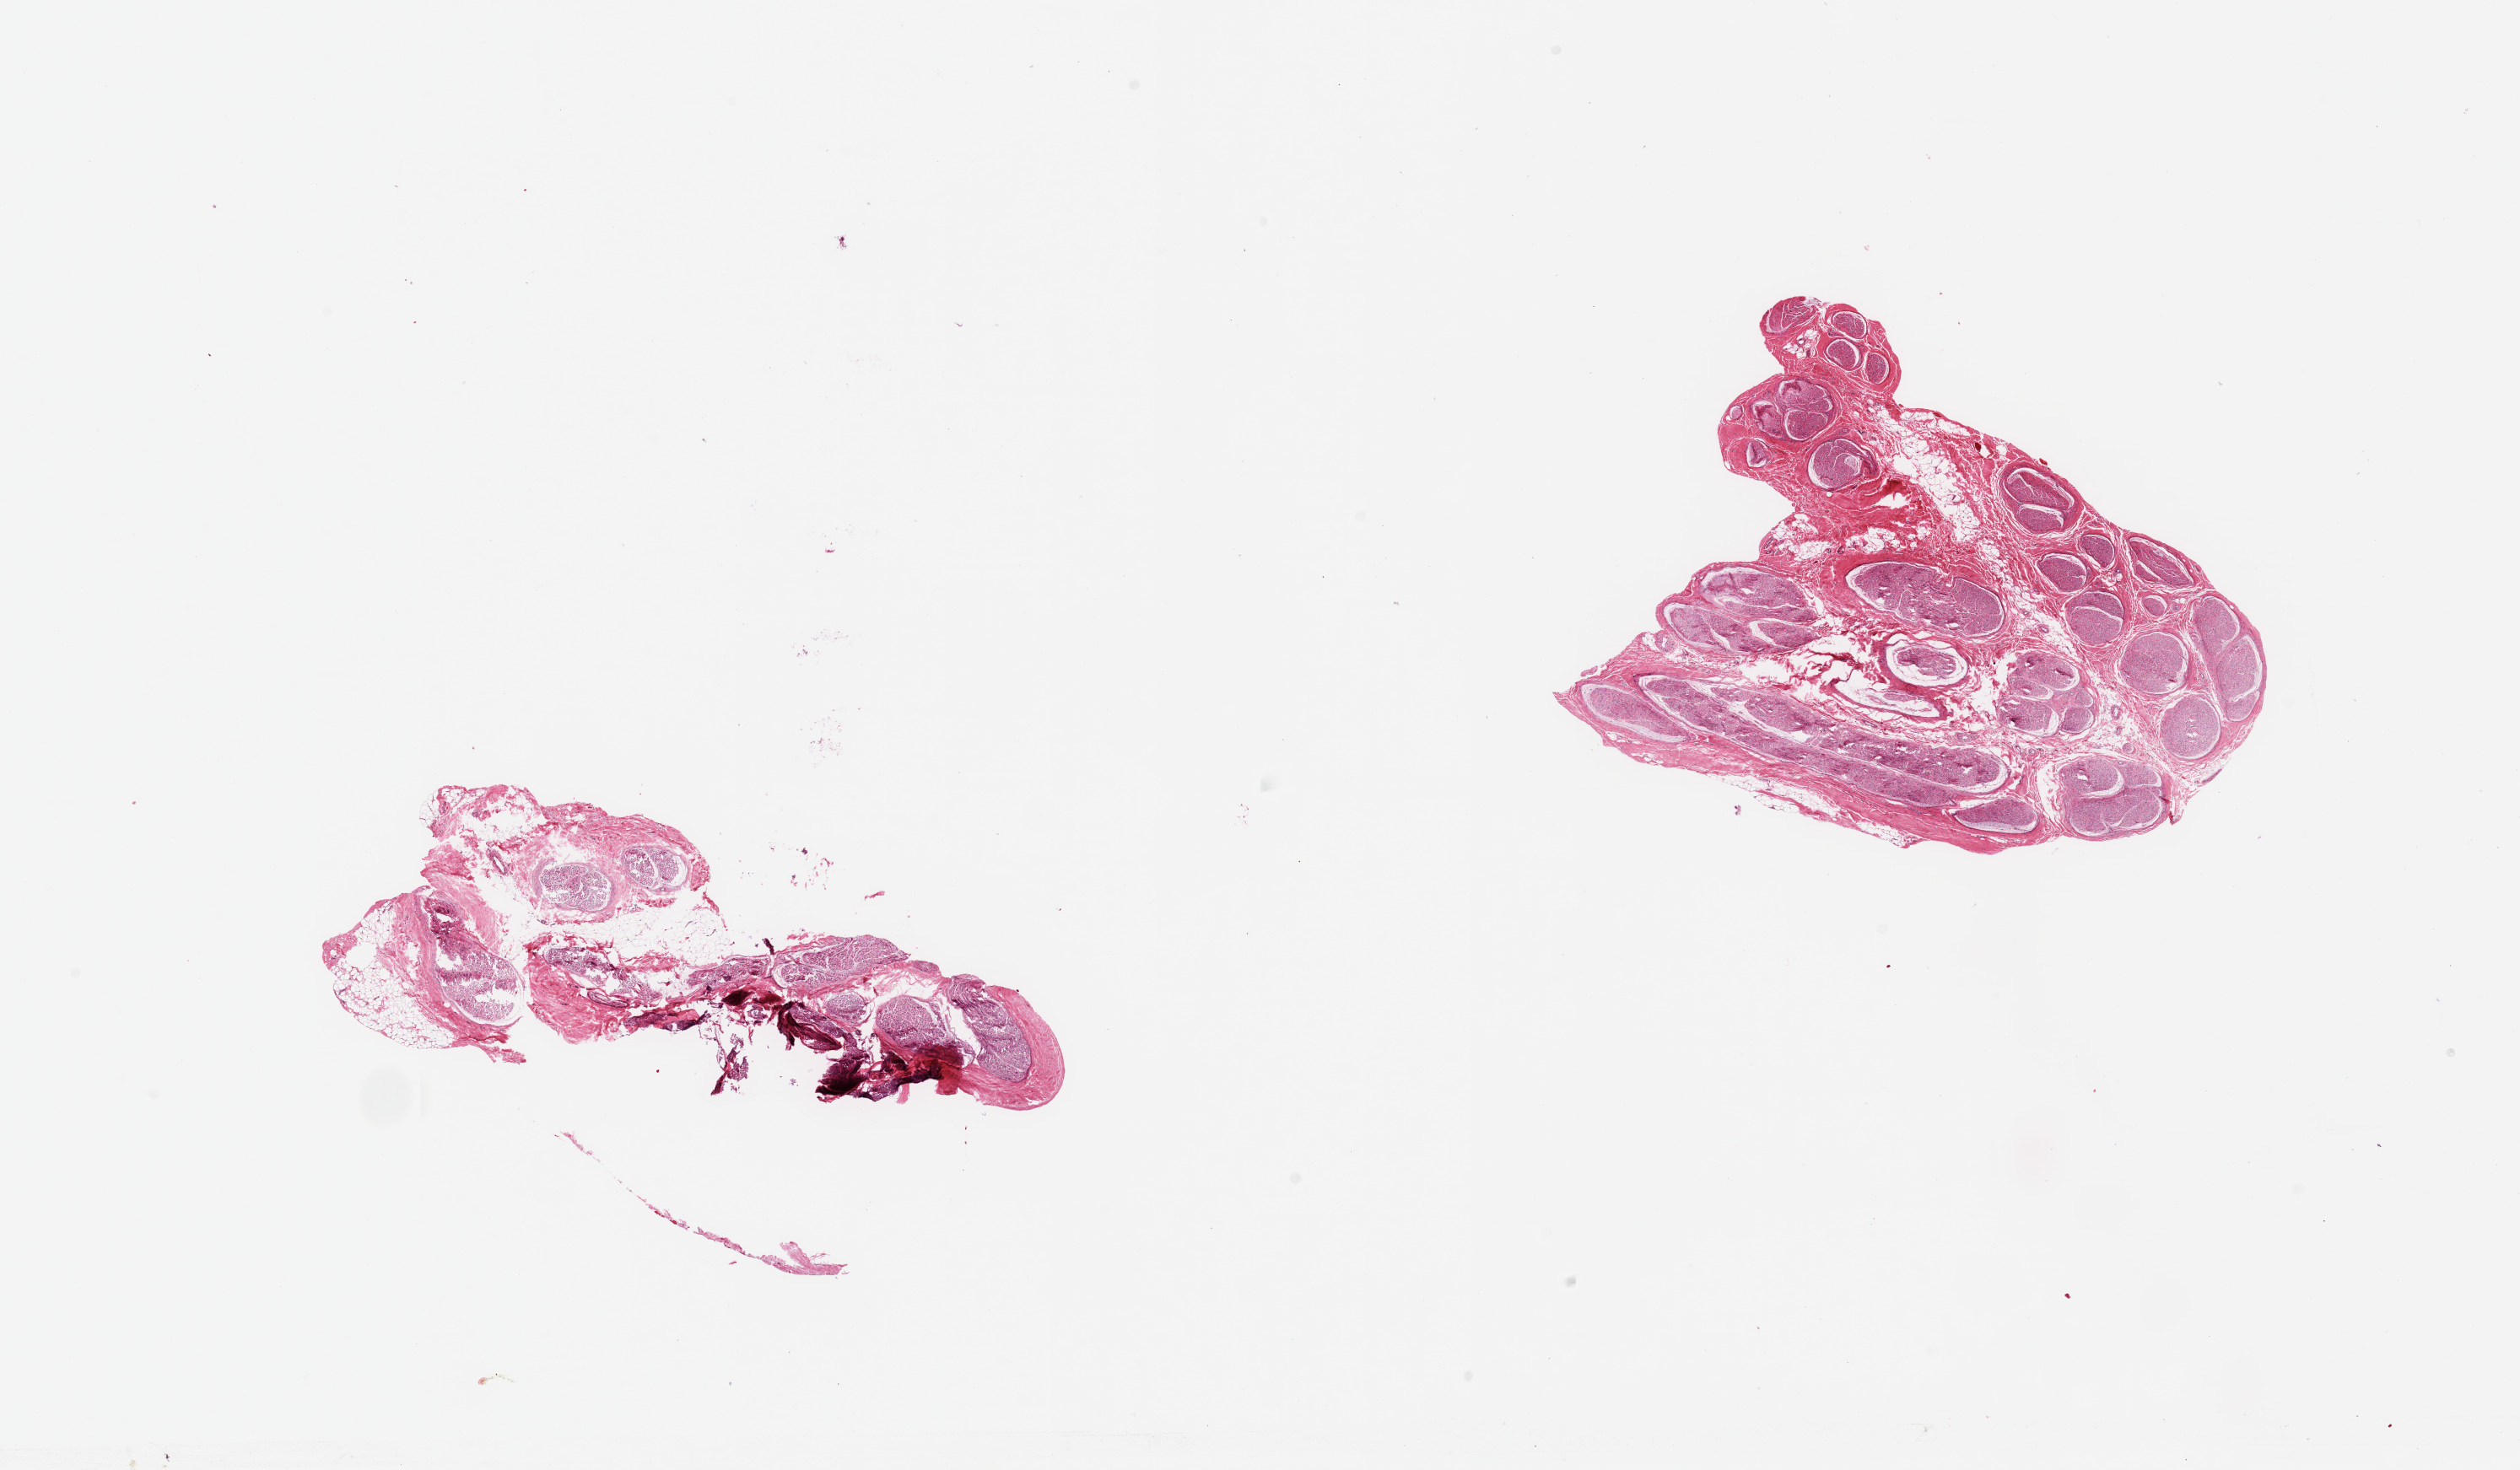
H&E whole-slide image, brightfield, whole scanned area (about 23.6 x 13.8 mm) shown as a low-resolution overview. PAXgene-fixed, paraffin-embedded tissue. Target tissue: tibial nerve. Tissue donor sample. Donor: male.
Pathologist's review note for this sample: 2 pieces; 1 with abundant external fibrofatty stroma.